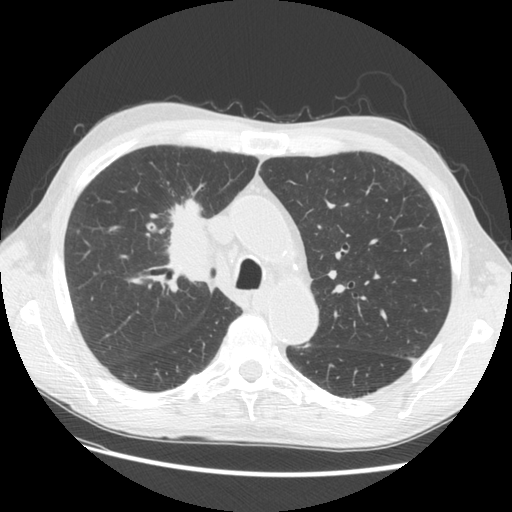
Chest CT (low-dose screening protocol), one axial image. Third annual screen. Lung window (W 1500 / L -600 HU). Standard (soft-tissue) reconstruction kernel (STANDARD). Slice 41 of 133 in the series. 512 × 512 image matrix. Male, age 73 years at enrolment.
• Expert reader's lesion annotation, box from (x=141, y=185) to (x=233, y=277) px.
• The screening reader recorded 4 non-calcified nodules or masses ≥4 mm on this exam (right upper lobe, right upper lobe, right upper lobe, left lower lobe); which of them this box marks is not recorded.
• Lung cancer was diagnosed 48 days after this screen: squamous cell carcinoma, NOS, right upper lobe, poorly differentiated (G3), stage IIIB (AJCC 6th edition), 56 mm at pathology.